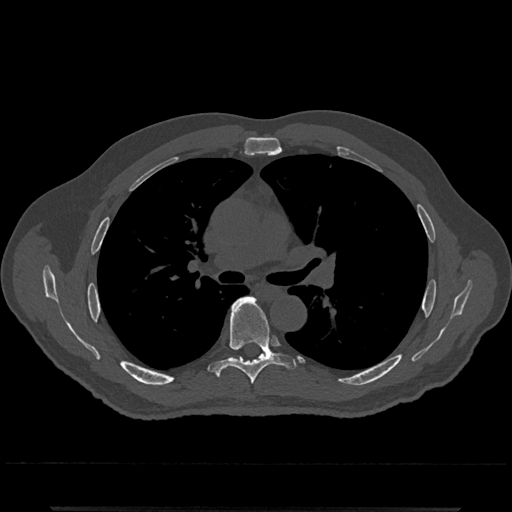
CT including the spine, one axial slice; position 774 of 797 along the scan axis; bone window (W 1800 / L 400 HU); 0.5 mm slice thickness; 512 × 512 image matrix. Male patient, age 67 years. From the clinical record (not read from this slice): primary cancer: prostate.
Outlined on this slice (semi-automatically segmented with operator editing):
- T6 vertebra: box from (x=208, y=297) to (x=295, y=385) px